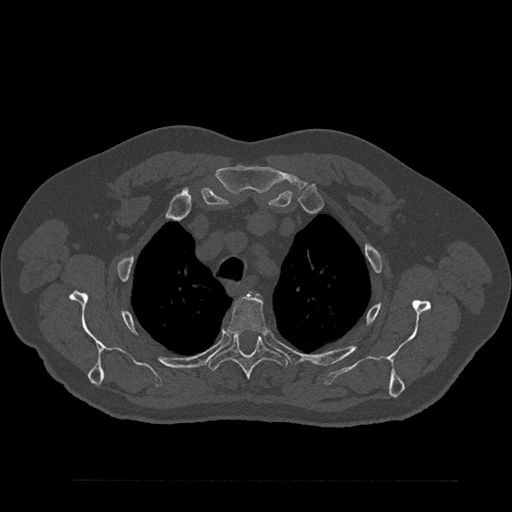
CT including the spine, one axial slice; position 661 of 797 along the scan axis; reconstruction kernel Br40s/3; bone window (W 1800 / L 400 HU); 512 × 512 image matrix. Patient: male, 61 years. Case-level facts recorded for this patient, not image findings: primary cancer: prostate.
Annotated regions visible in this slice (semi-automatically segmented with operator editing):
- T3 vertebra: box from (x=228, y=296) to (x=267, y=335) px
- T4 vertebra: (x=207, y=333)–(x=288, y=380)